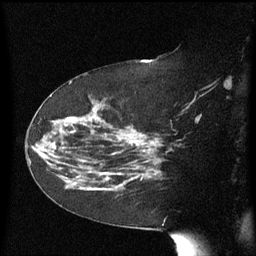
Breast MRI (dynamic contrast-enhanced), one sagittal slice; dynamic contrast-enhanced series, image 2 of 3 at this slice position (ordered by acquisition); 1.5 T; TE 4.2 ms, TR 8.4 ms; 2.3 mm slice thickness; 256 × 256 image matrix, field of view 200 × 200 mm. Patient: female, 63 years. Case-level facts recorded for this patient, not image findings: setting: breast cancer imaged before/during neoadjuvant chemotherapy; receptor status: HER2-positive.
Annotated regions visible in this slice (semi-automatically segmented with operator editing):
- analysis volume of interest (the breast-tissue region the enhancement analysis was run in; not a lesion): bounding box <63,144,147,196> (left, top, right, bottom; pixels)
- tumour enhancement mask (voxels above the 70 % enhancement threshold inside the analysis volume of interest): <97,144,146,177>